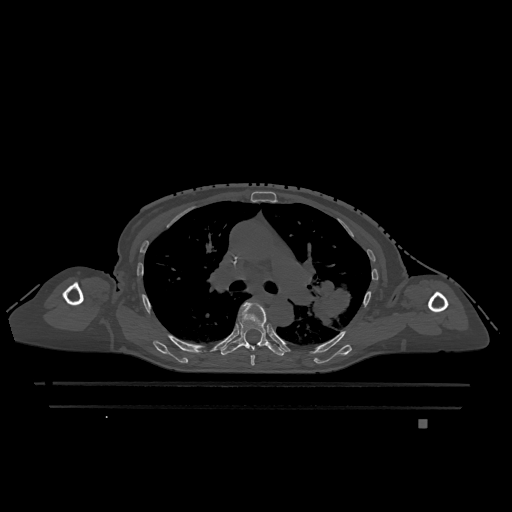
CT including the spine, one axial slice; slice 805 of 1317 in the series (ordered by position); bone window (W 1800 / L 400 HU); 512 × 512 image matrix, field of view 500 × 500 mm. Female patient, age 74 years. Case-level facts recorded for this patient, not image findings: primary cancer: lung.
Structures marked on this image (semi-automatic segmentation, software-assisted and operator-edited):
- T5 vertebra: bounding box (x1, y1, x2, y2) in pixels: (251, 355, 255, 366)
- T6 vertebra: (221, 302, 284, 356)